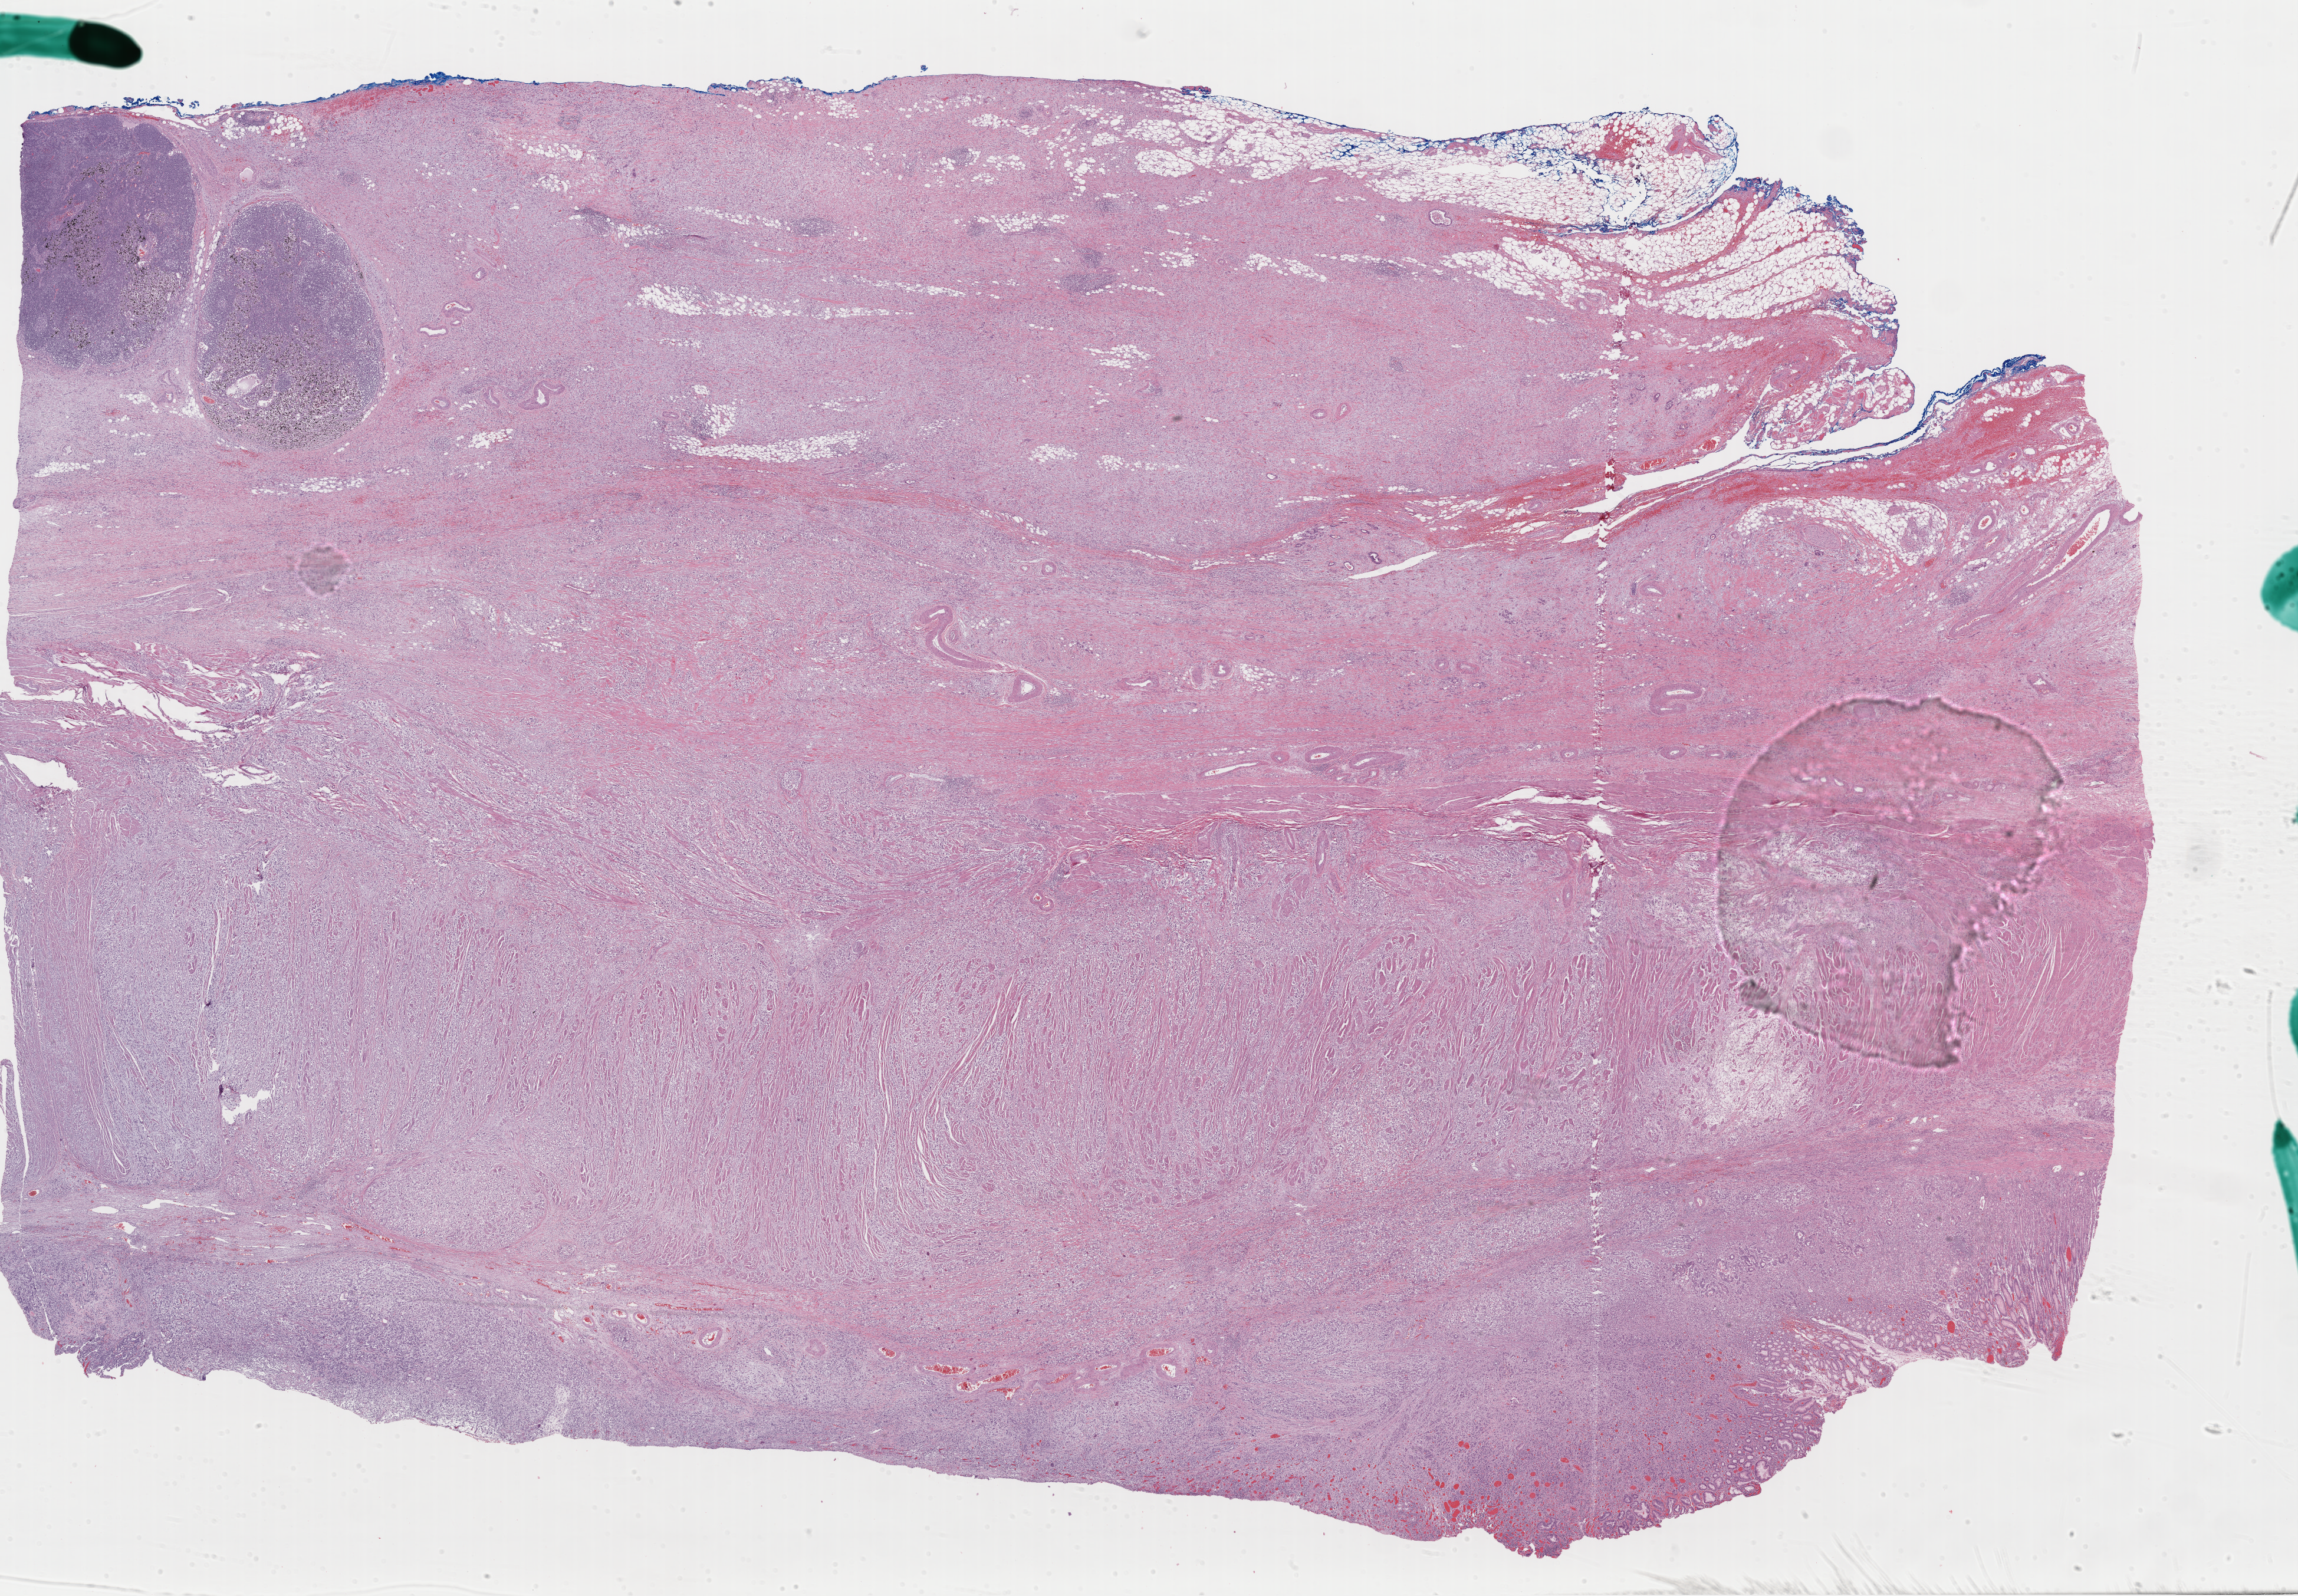
Digitized Hematoxylin and eosin (H&E) stained tissue section (whole slide), whole scanned area (about 30.8 x 21.4 mm, acquisition: 40x scan) shown as a low-resolution overview, formalin-fixed paraffin-embedded (FFPE) diagnostic section, sample: primary tumour, esophagus. Patient: male, age at initial diagnosis 77 years. Histologic grade: GX (grade cannot be assessed).
• AJCC pathologic stage: IV
• histologic diagnosis: Adenocarcinoma, NOS